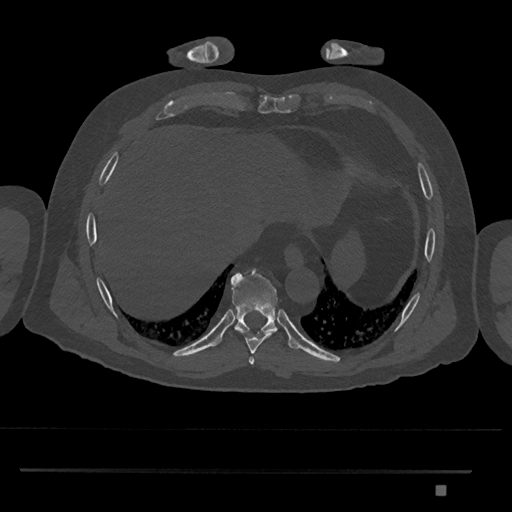
CT including the spine, one axial slice; position 1081 of 1134 along the scan axis; 120 kVp; bone window (W 1800 / L 400 HU); 0.5 mm slice thickness; 512 × 512 image matrix, field of view 429 × 429 mm. Patient: male, 65 years. From the clinical record (not read from this slice): primary cancer: prostate.
Structures marked on this image (semi-automatically segmented with operator editing):
- T8 vertebra: box from (x=235, y=330) to (x=276, y=355) px
- T9 vertebra: (x=231, y=269)–(x=278, y=334)